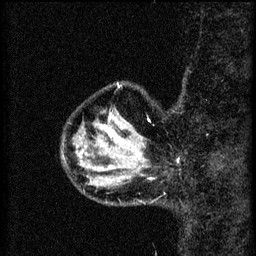
Breast MRI (dynamic contrast-enhanced), one sagittal slice. Slice 12 of 60 in the series (ordered by position). 3 images stored at this slice position (order not interpretable as contrast timing). 1.5 T. TE 4.2 ms, TR 8.2 ms. 2 mm slice thickness. 256 × 256 image matrix, field of view 180 × 180 mm. Patient: female, 37 years.
Structures marked on this image (semi-automatic segmentation, software-assisted and operator-edited):
- analysis volume of interest (the breast-tissue region the enhancement analysis was run in; not a lesion): bounding box <124,138,181,179> (left, top, right, bottom; pixels)
- tumour enhancement mask (voxels above the 70 % enhancement threshold inside the analysis volume of interest): <138,154,179,161>